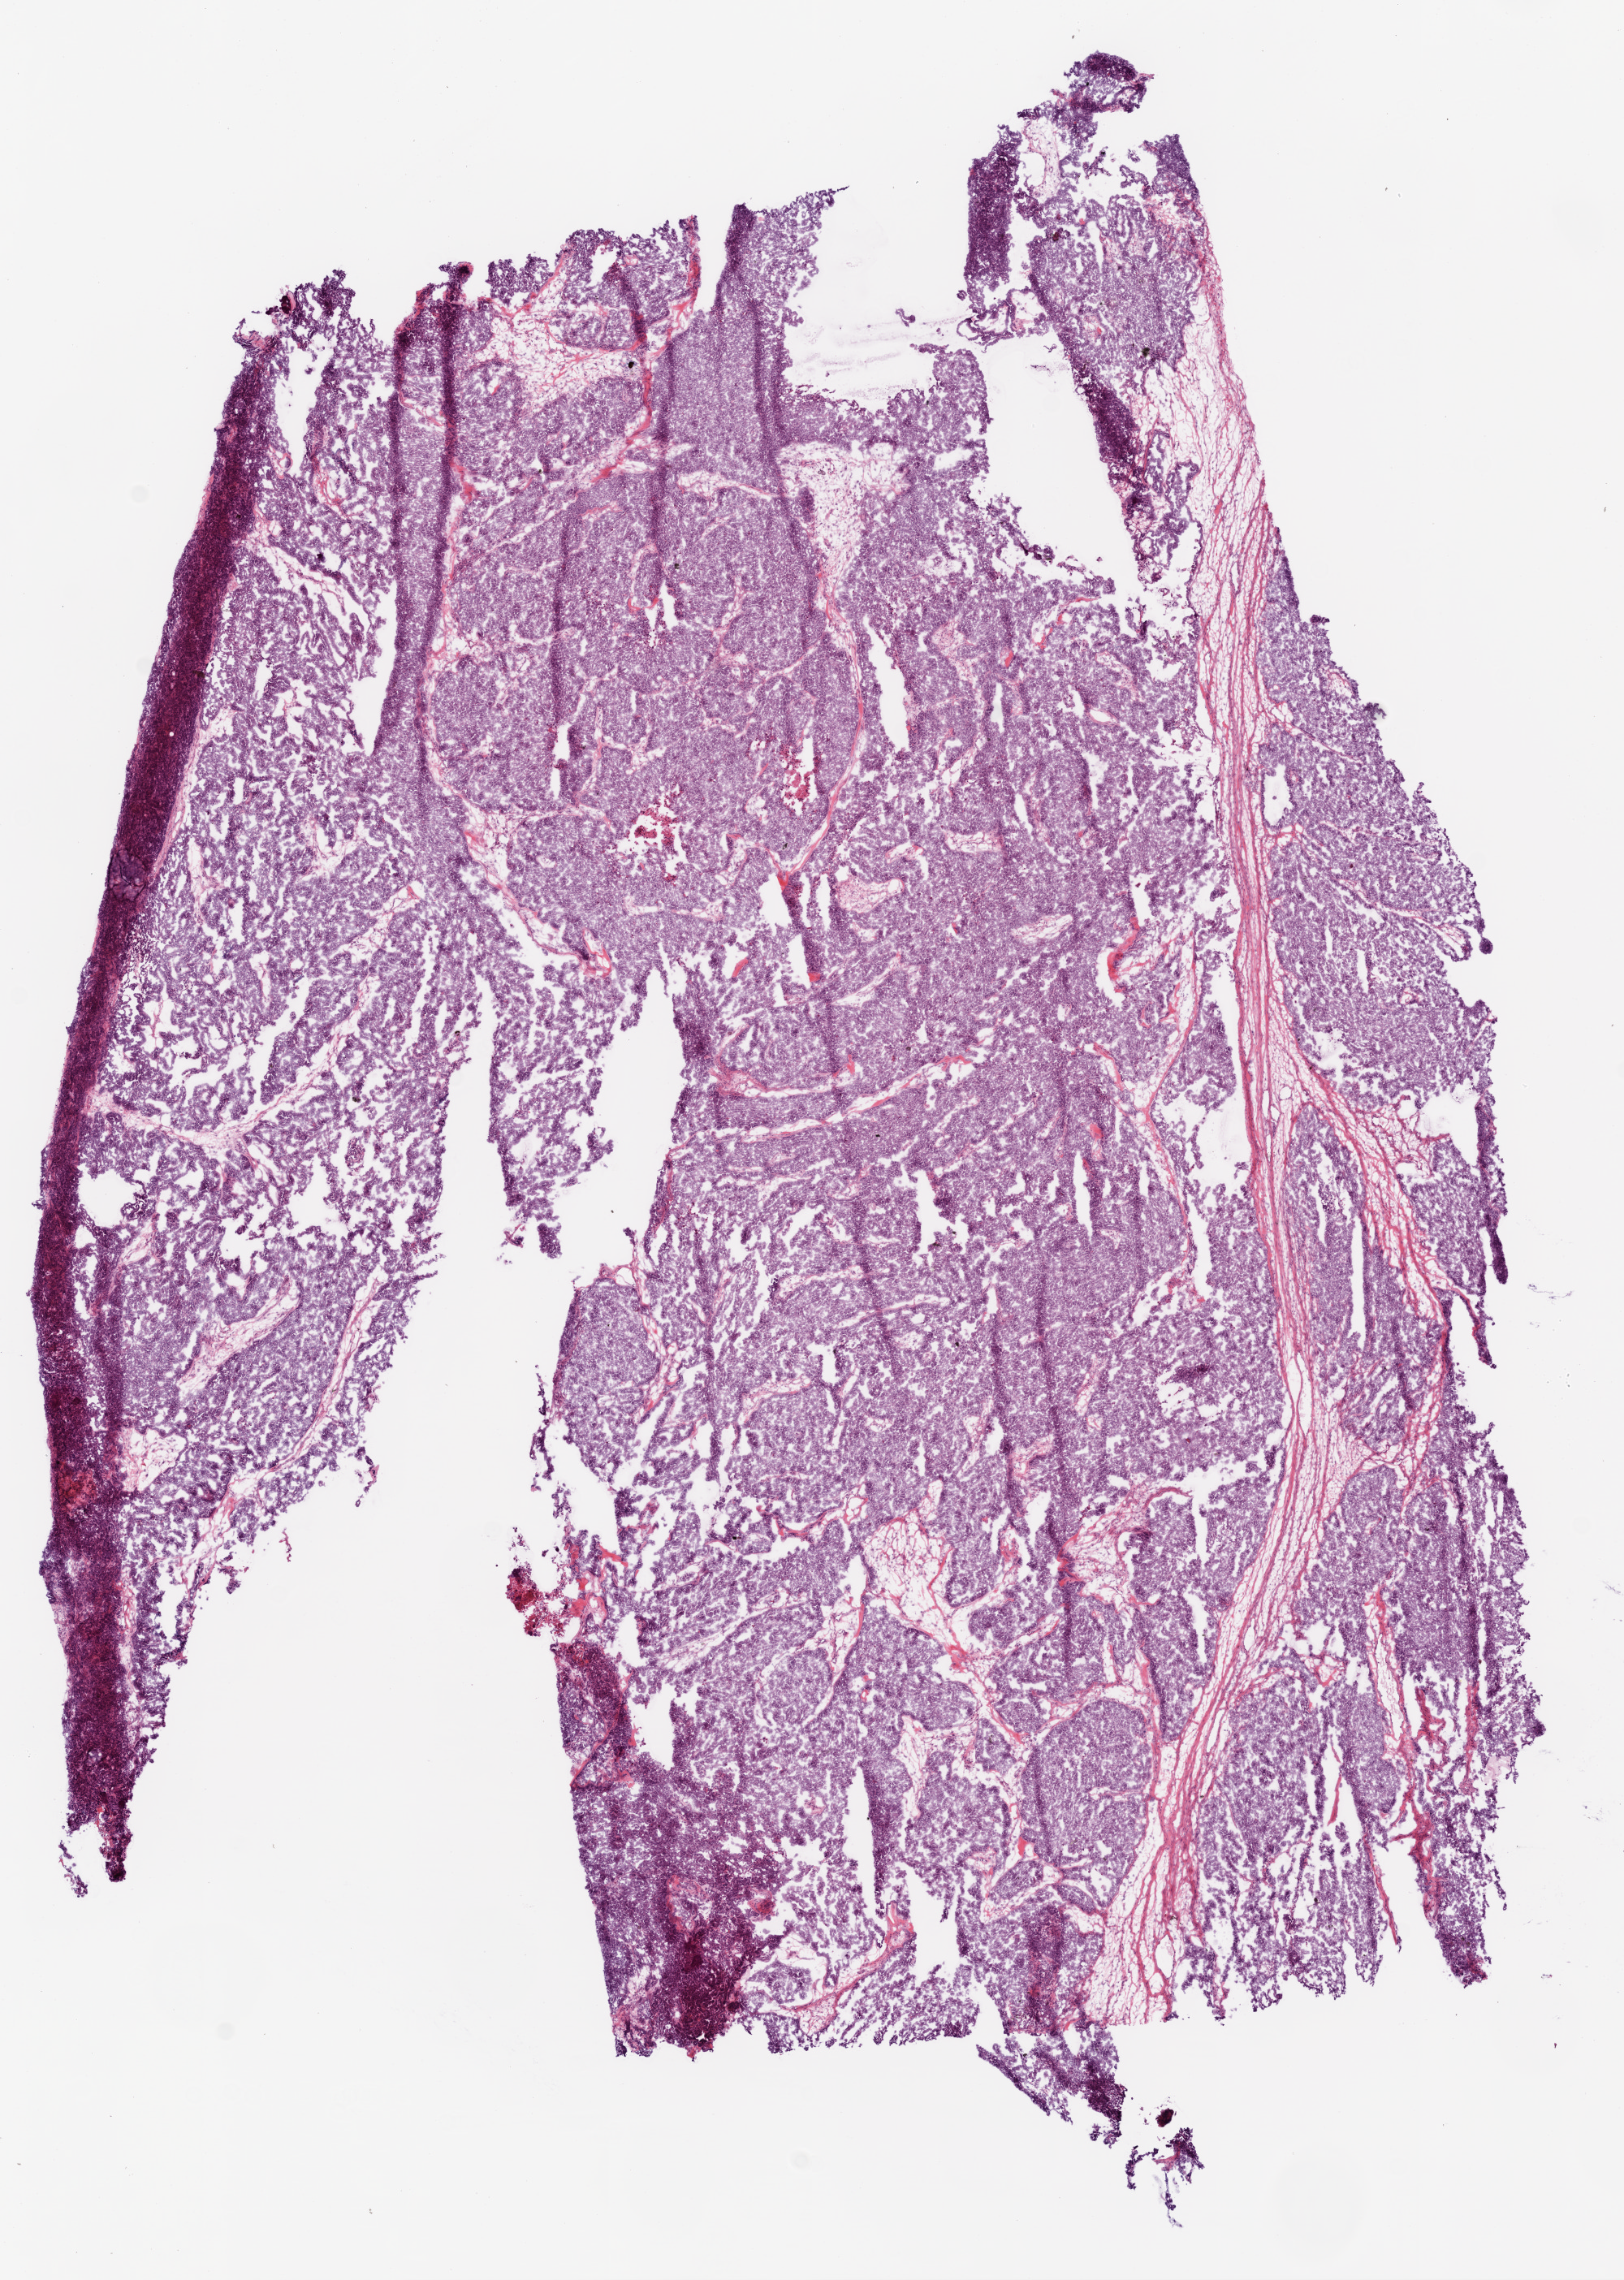
Digitized H&E tissue section (whole slide) — shown as a low-resolution overview of the whole scanned area (about 8.0 x 11.3 mm, acquisition: 20x scan), frozen section from the bottom of the tissue portion, ovary, primary tumour sample. Female patient; age at initial diagnosis 73 years.
Diagnosis: Serous cystadenocarcinoma, NOS.